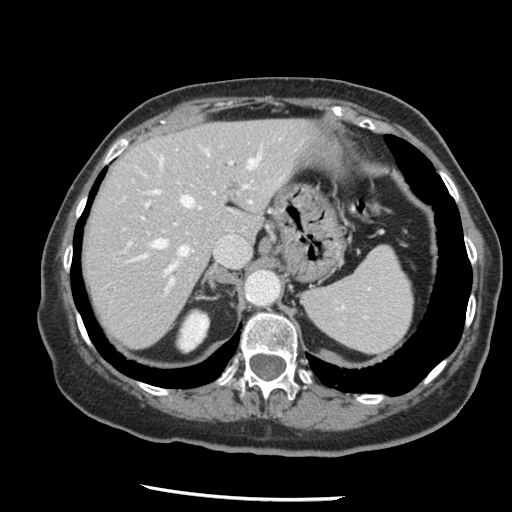
Contrast-enhanced abdominal CT, one axial slice. Position 100 of 148 along the scan axis. Intravenous contrast given. Soft-tissue window (W 400 / L 40 HU). 512 × 512 image matrix, field of view 330 × 330 mm. Female patient, age 85 years. Case-level facts recorded for this patient, not image findings: diagnosis: colorectal cancer liver metastases, imaged before liver resection; multiple liver metastases: no; largest metastasis: 0.9 cm; chemotherapy before resection: yes.
Annotated regions visible in this slice (manually delineated by an expert):
- hepatic veins: bounding box <121,144,263,272> (left, top, right, bottom; pixels)
- liver: <83,120,315,348>
- planned liver remnant (the part of the liver to remain after resection): <83,120,315,348>
- portal vein (with intrahepatic branches): <128,160,249,296>